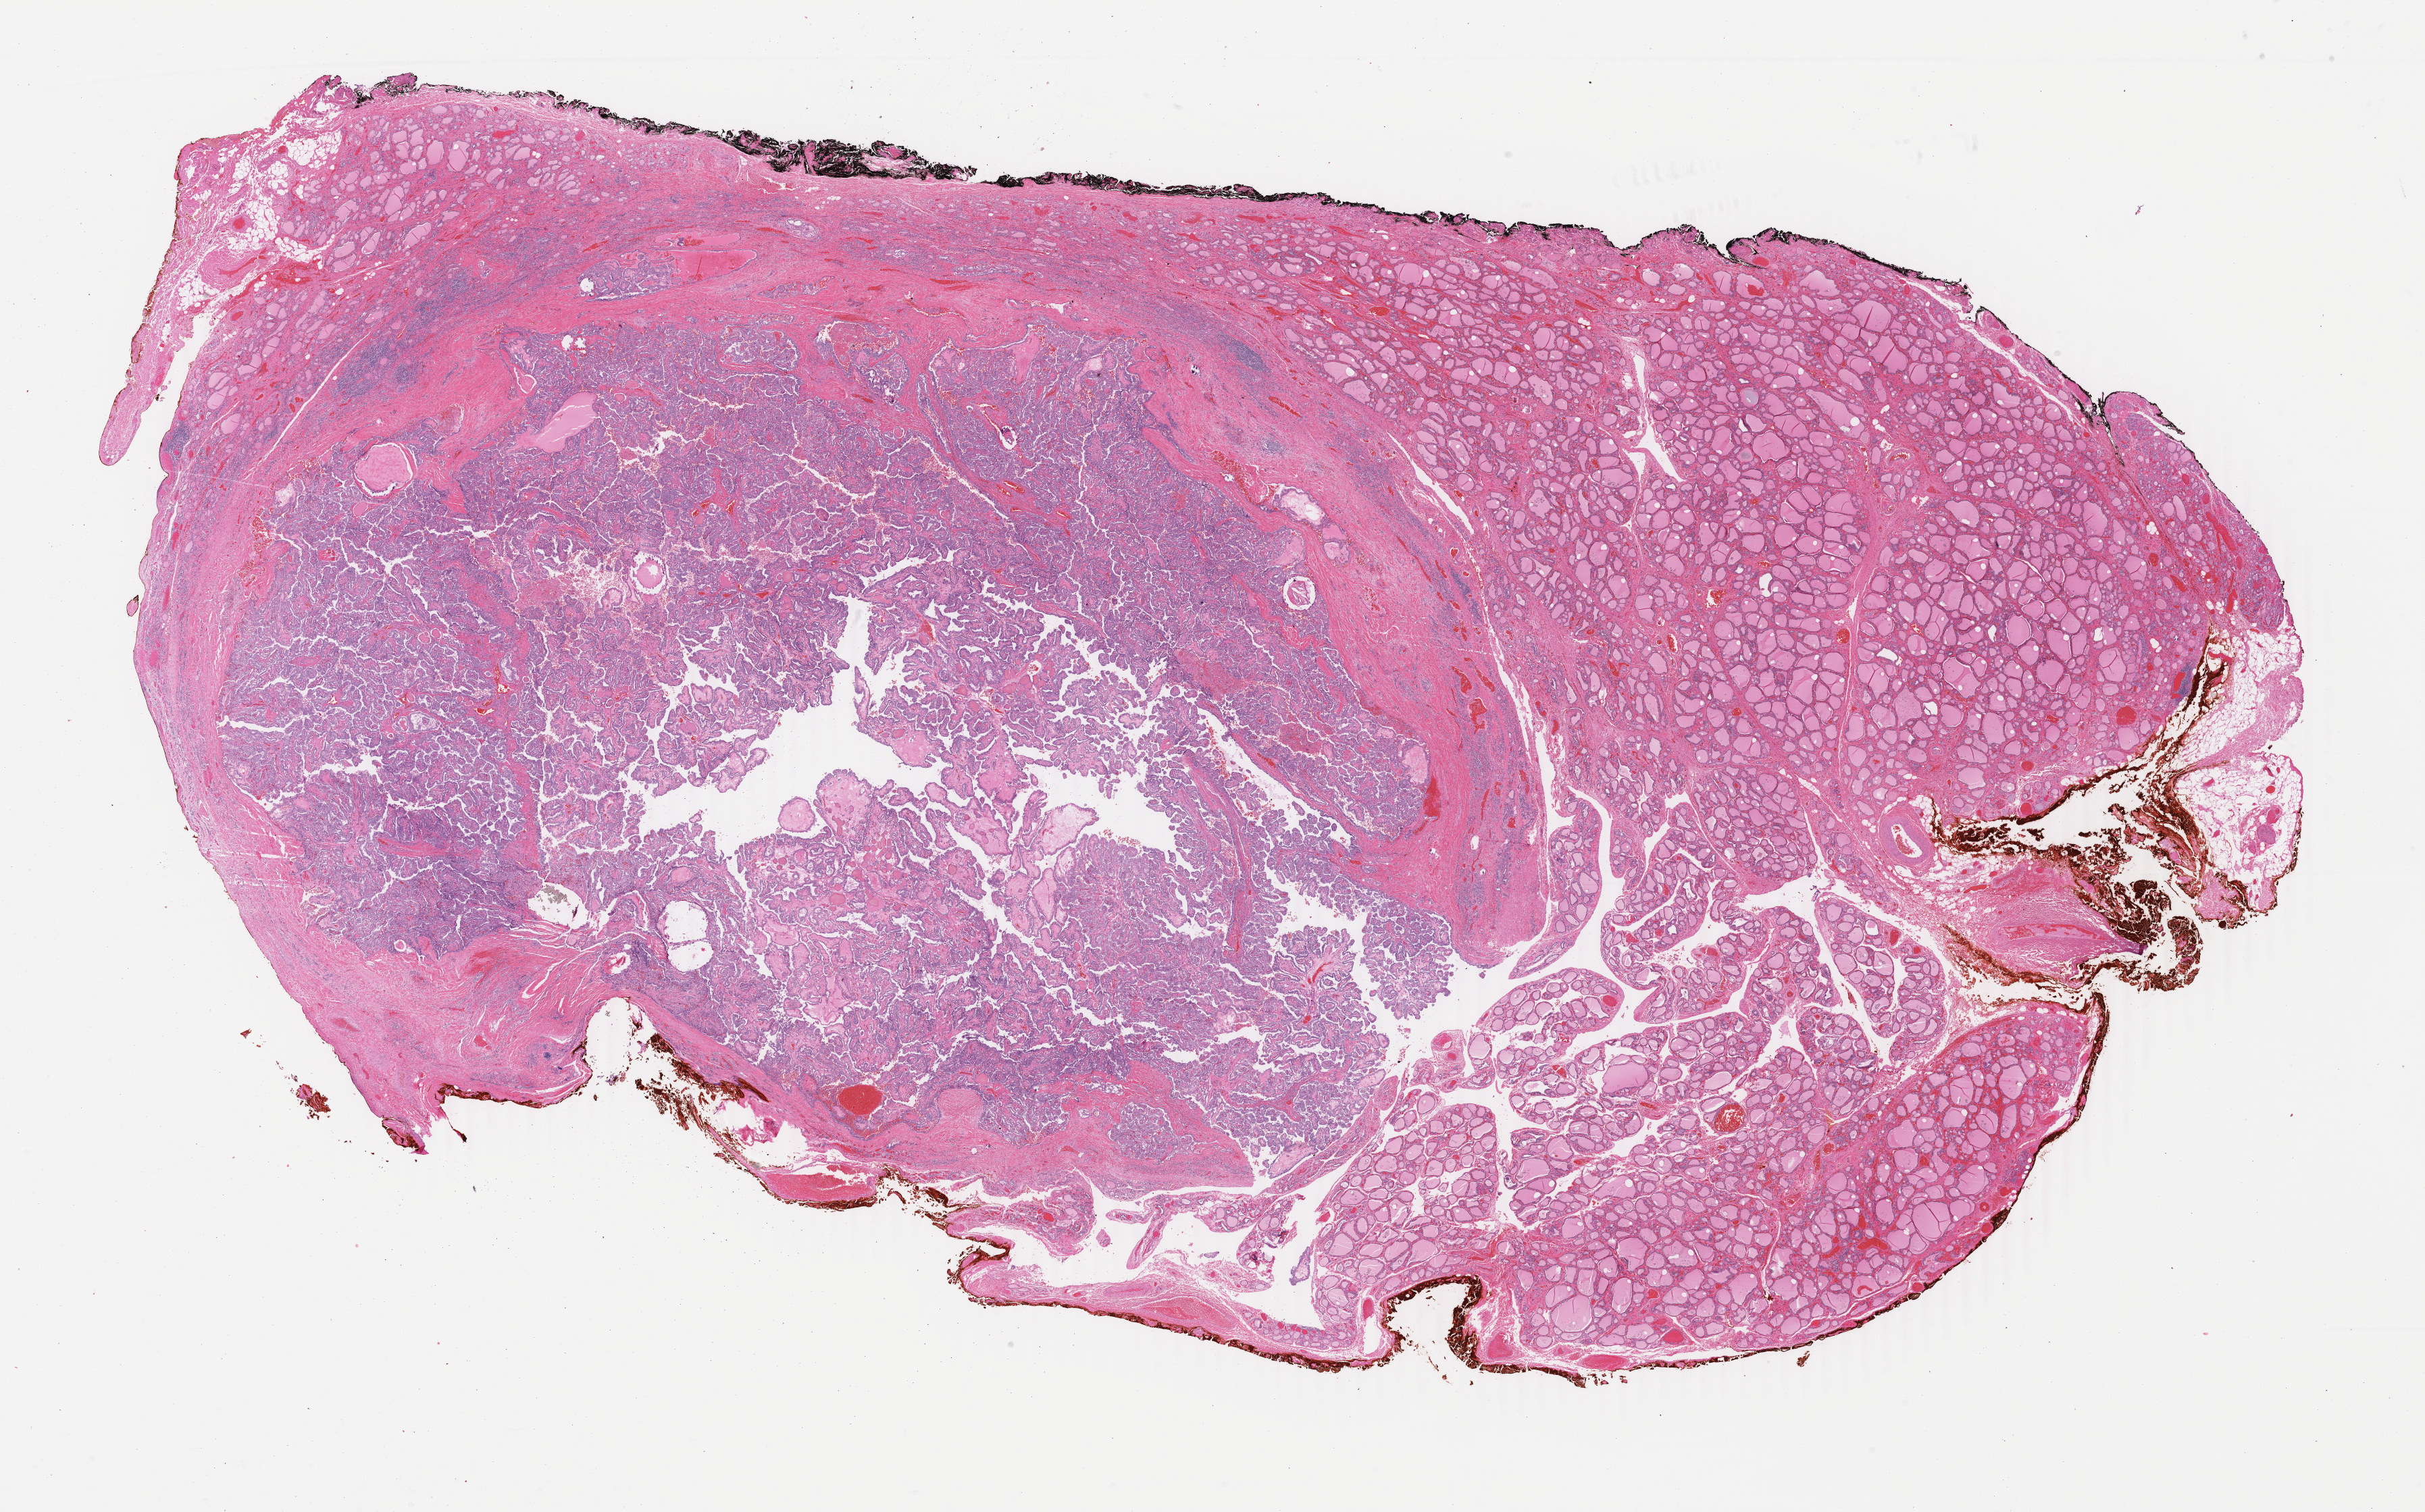
Whole-slide histology image, H&E-stained — shown as a low-resolution overview of the whole scanned area (about 28.6 x 17.8 mm, from a 40x scan); formalin-fixed paraffin-embedded (FFPE) diagnostic section; primary tumour sample from the thyroid. Patient: female, age at initial diagnosis 36 years.
Diagnosis: Papillary adenocarcinoma, NOS (thyroid gland). Laterality: right. AJCC pathologic stage: I (6th edition). TNM: T2 N1a MX.